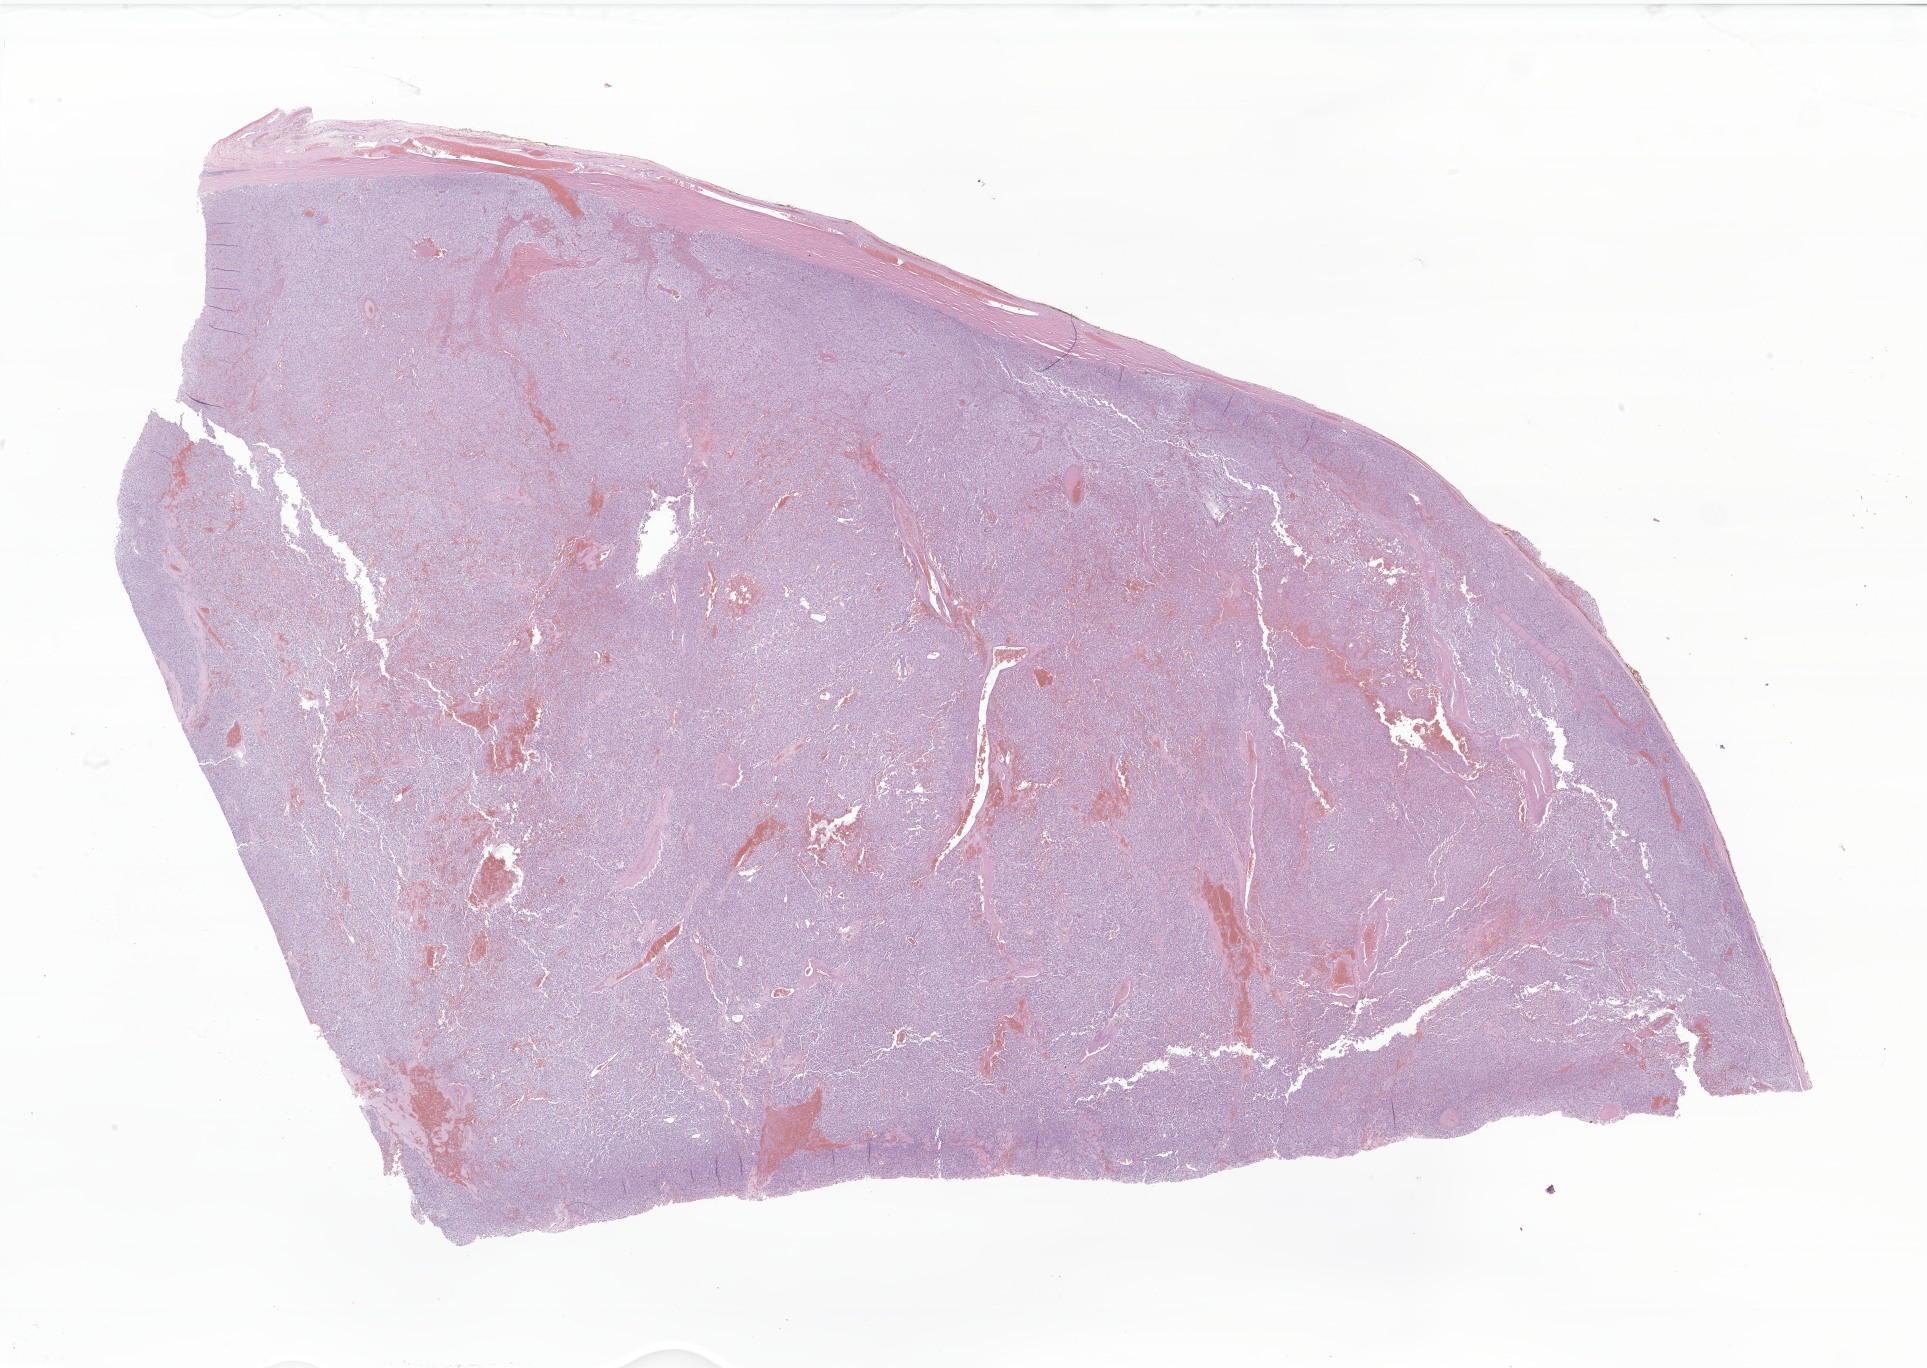
Whole-slide image, H&E stain of tumor tissue from the abdomen, low-resolution overview of the scanned area, about 32.5 x 23.1 mm. FFPE section. Patient: male, age 281 months (23 years 5 months).
Diagnosis: Sympathetic paraganglioma.